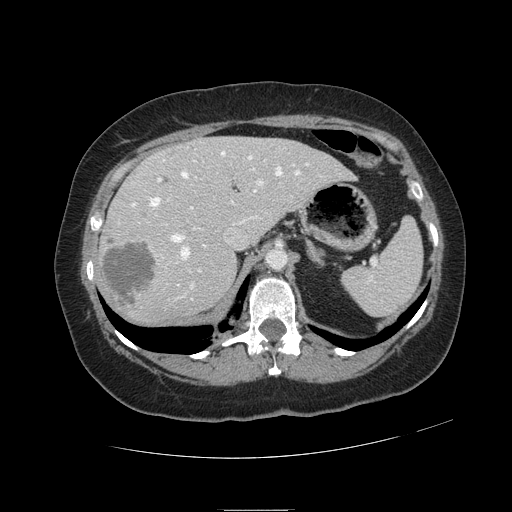
Contrast-enhanced abdominal CT, one axial slice; slice 78 of 121 in the series (ordered by position); 120 kVp; soft-tissue window (W 400 / L 40 HU); 2.5 mm slice thickness; 512 × 512 image matrix, field of view 400 × 400 mm. Female patient, age 52 years. Case-level facts recorded for this patient, not image findings: diagnosis: colorectal cancer liver metastases, imaged before liver resection; multiple liver metastases: yes; largest metastasis: 6.3 cm.
Outlined on this slice (outlined manually by an expert reader):
- hepatic veins: bounding box <132,151,309,286> (left, top, right, bottom; pixels)
- liver: <100,137,351,323>
- planned liver remnant (the part of the liver to remain after resection): <168,137,350,238>
- portal vein (with intrahepatic branches): <158,160,266,299>
- liver metastasis: <104,239,156,305>